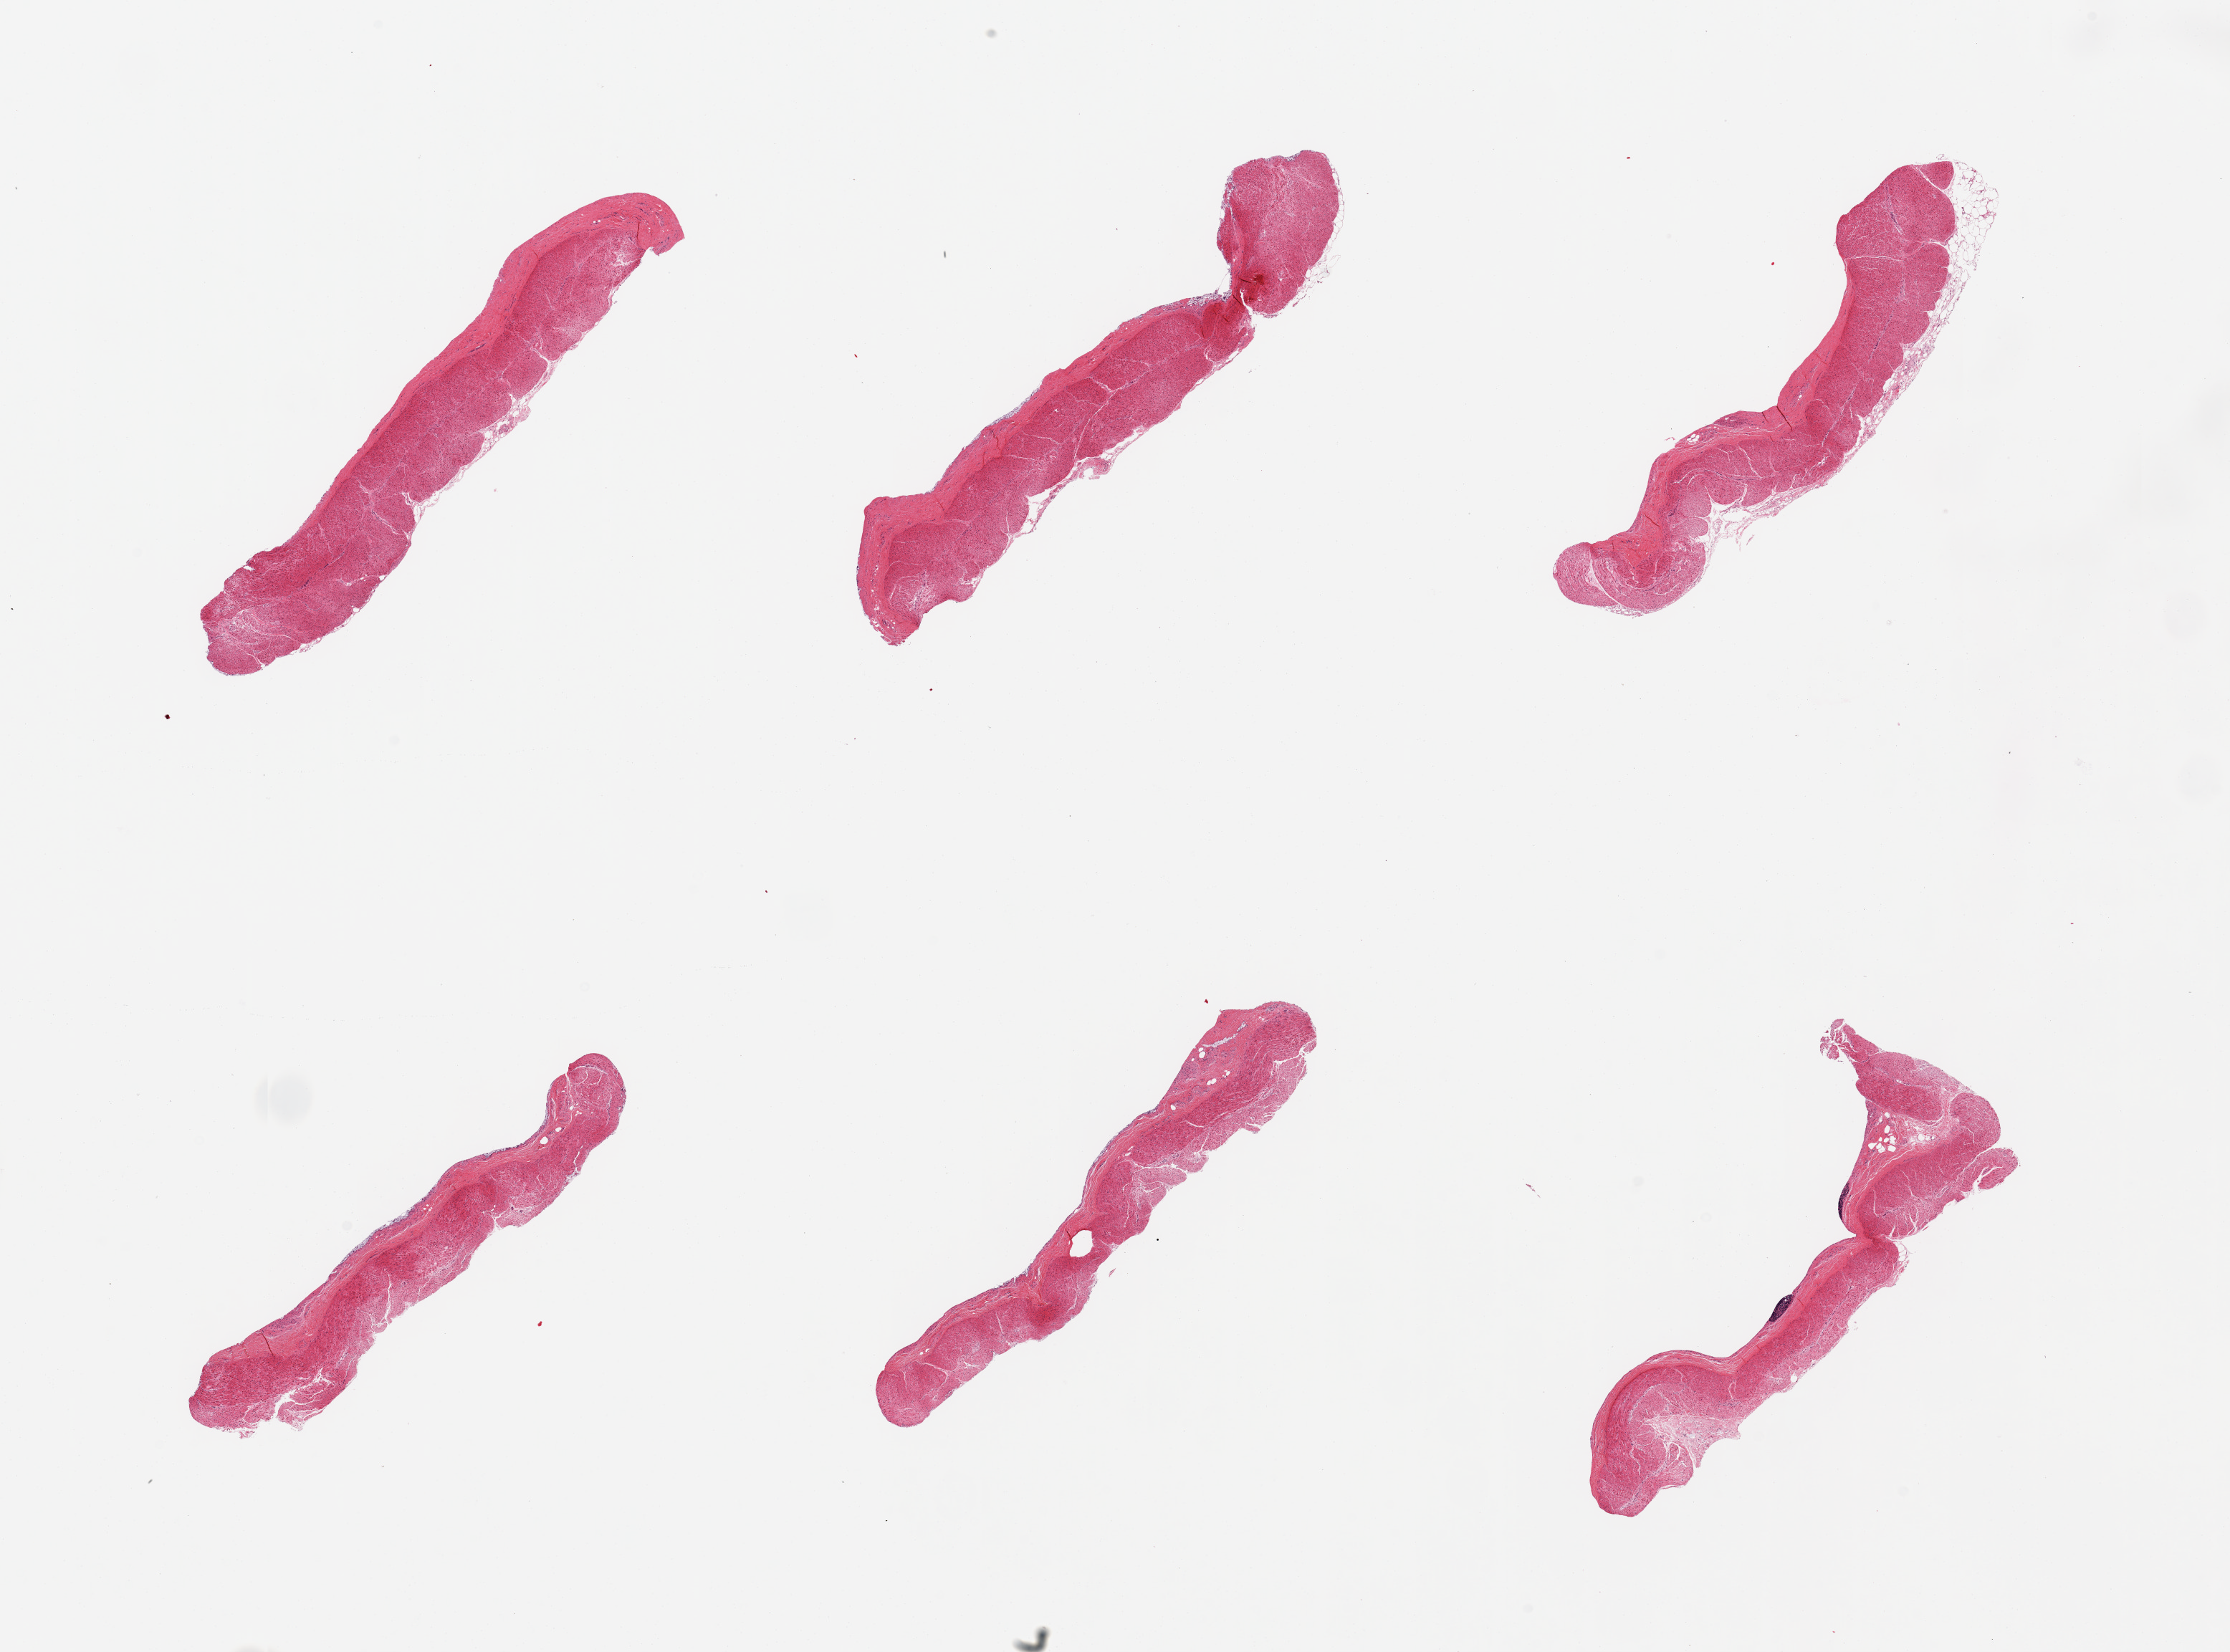
Digitized haematoxylin and eosin-stained section, brightfield, whole scanned area (about 24.6 x 18.2 mm, slide scanned at 20x) shown as a low-resolution overview. PAXgene-fixed paraffin-embedded (PFPE) section. Sampled site (target tissue): sigmoid colon. Tissue donor sample. Male donor.
Pathologist's review note for this sample: 6 pieces; predominantly well trimmed, few residual lymphoid aggregates.